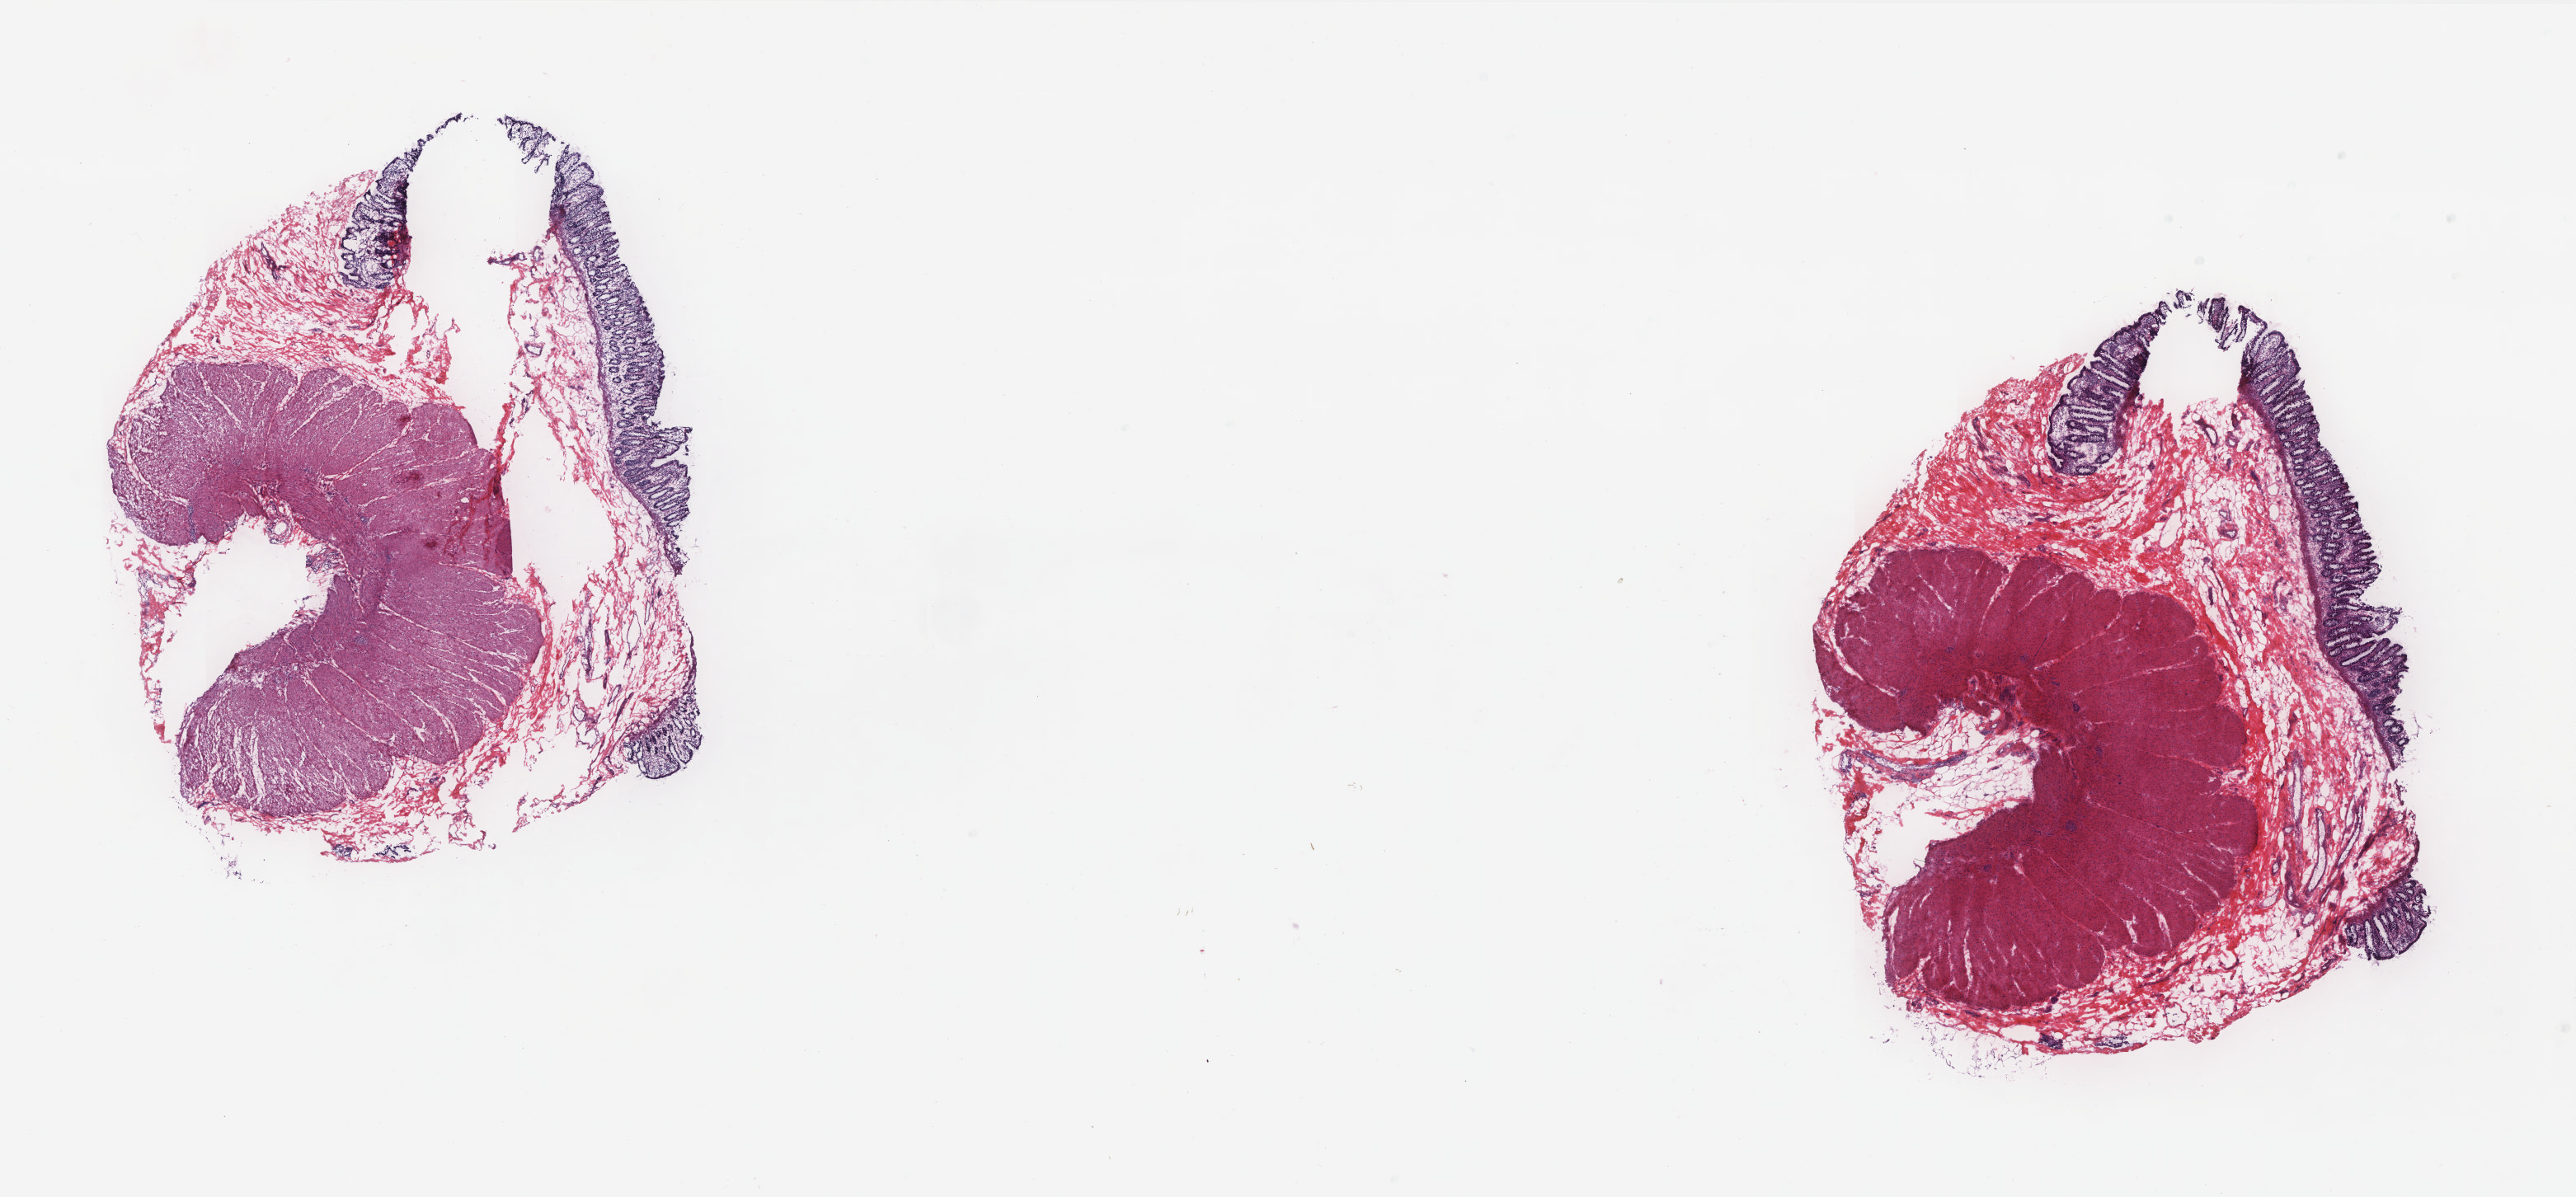
Whole-slide histology image, Hematoxylin and eosin (H&E) stained, low-resolution overview of the scanned area, about 25.0 x 11.6 mm (slide scanned at 20x); frozen section from the top of the tissue portion; solid tissue normal (non-tumour tissue) sample from the rectum. Patient: female, age at initial diagnosis 67 years. Slide review estimates, as recorded: tumour cells 0%, normal cells 100%. Inflammatory infiltration, as recorded: lymphocyte infiltration 25%, monocyte infiltration 5%, neutrophil infiltration 0%.
This section: solid tissue normal (non-tumour) sample from the same patient. Patient diagnosis: Adenocarcinoma, NOS.